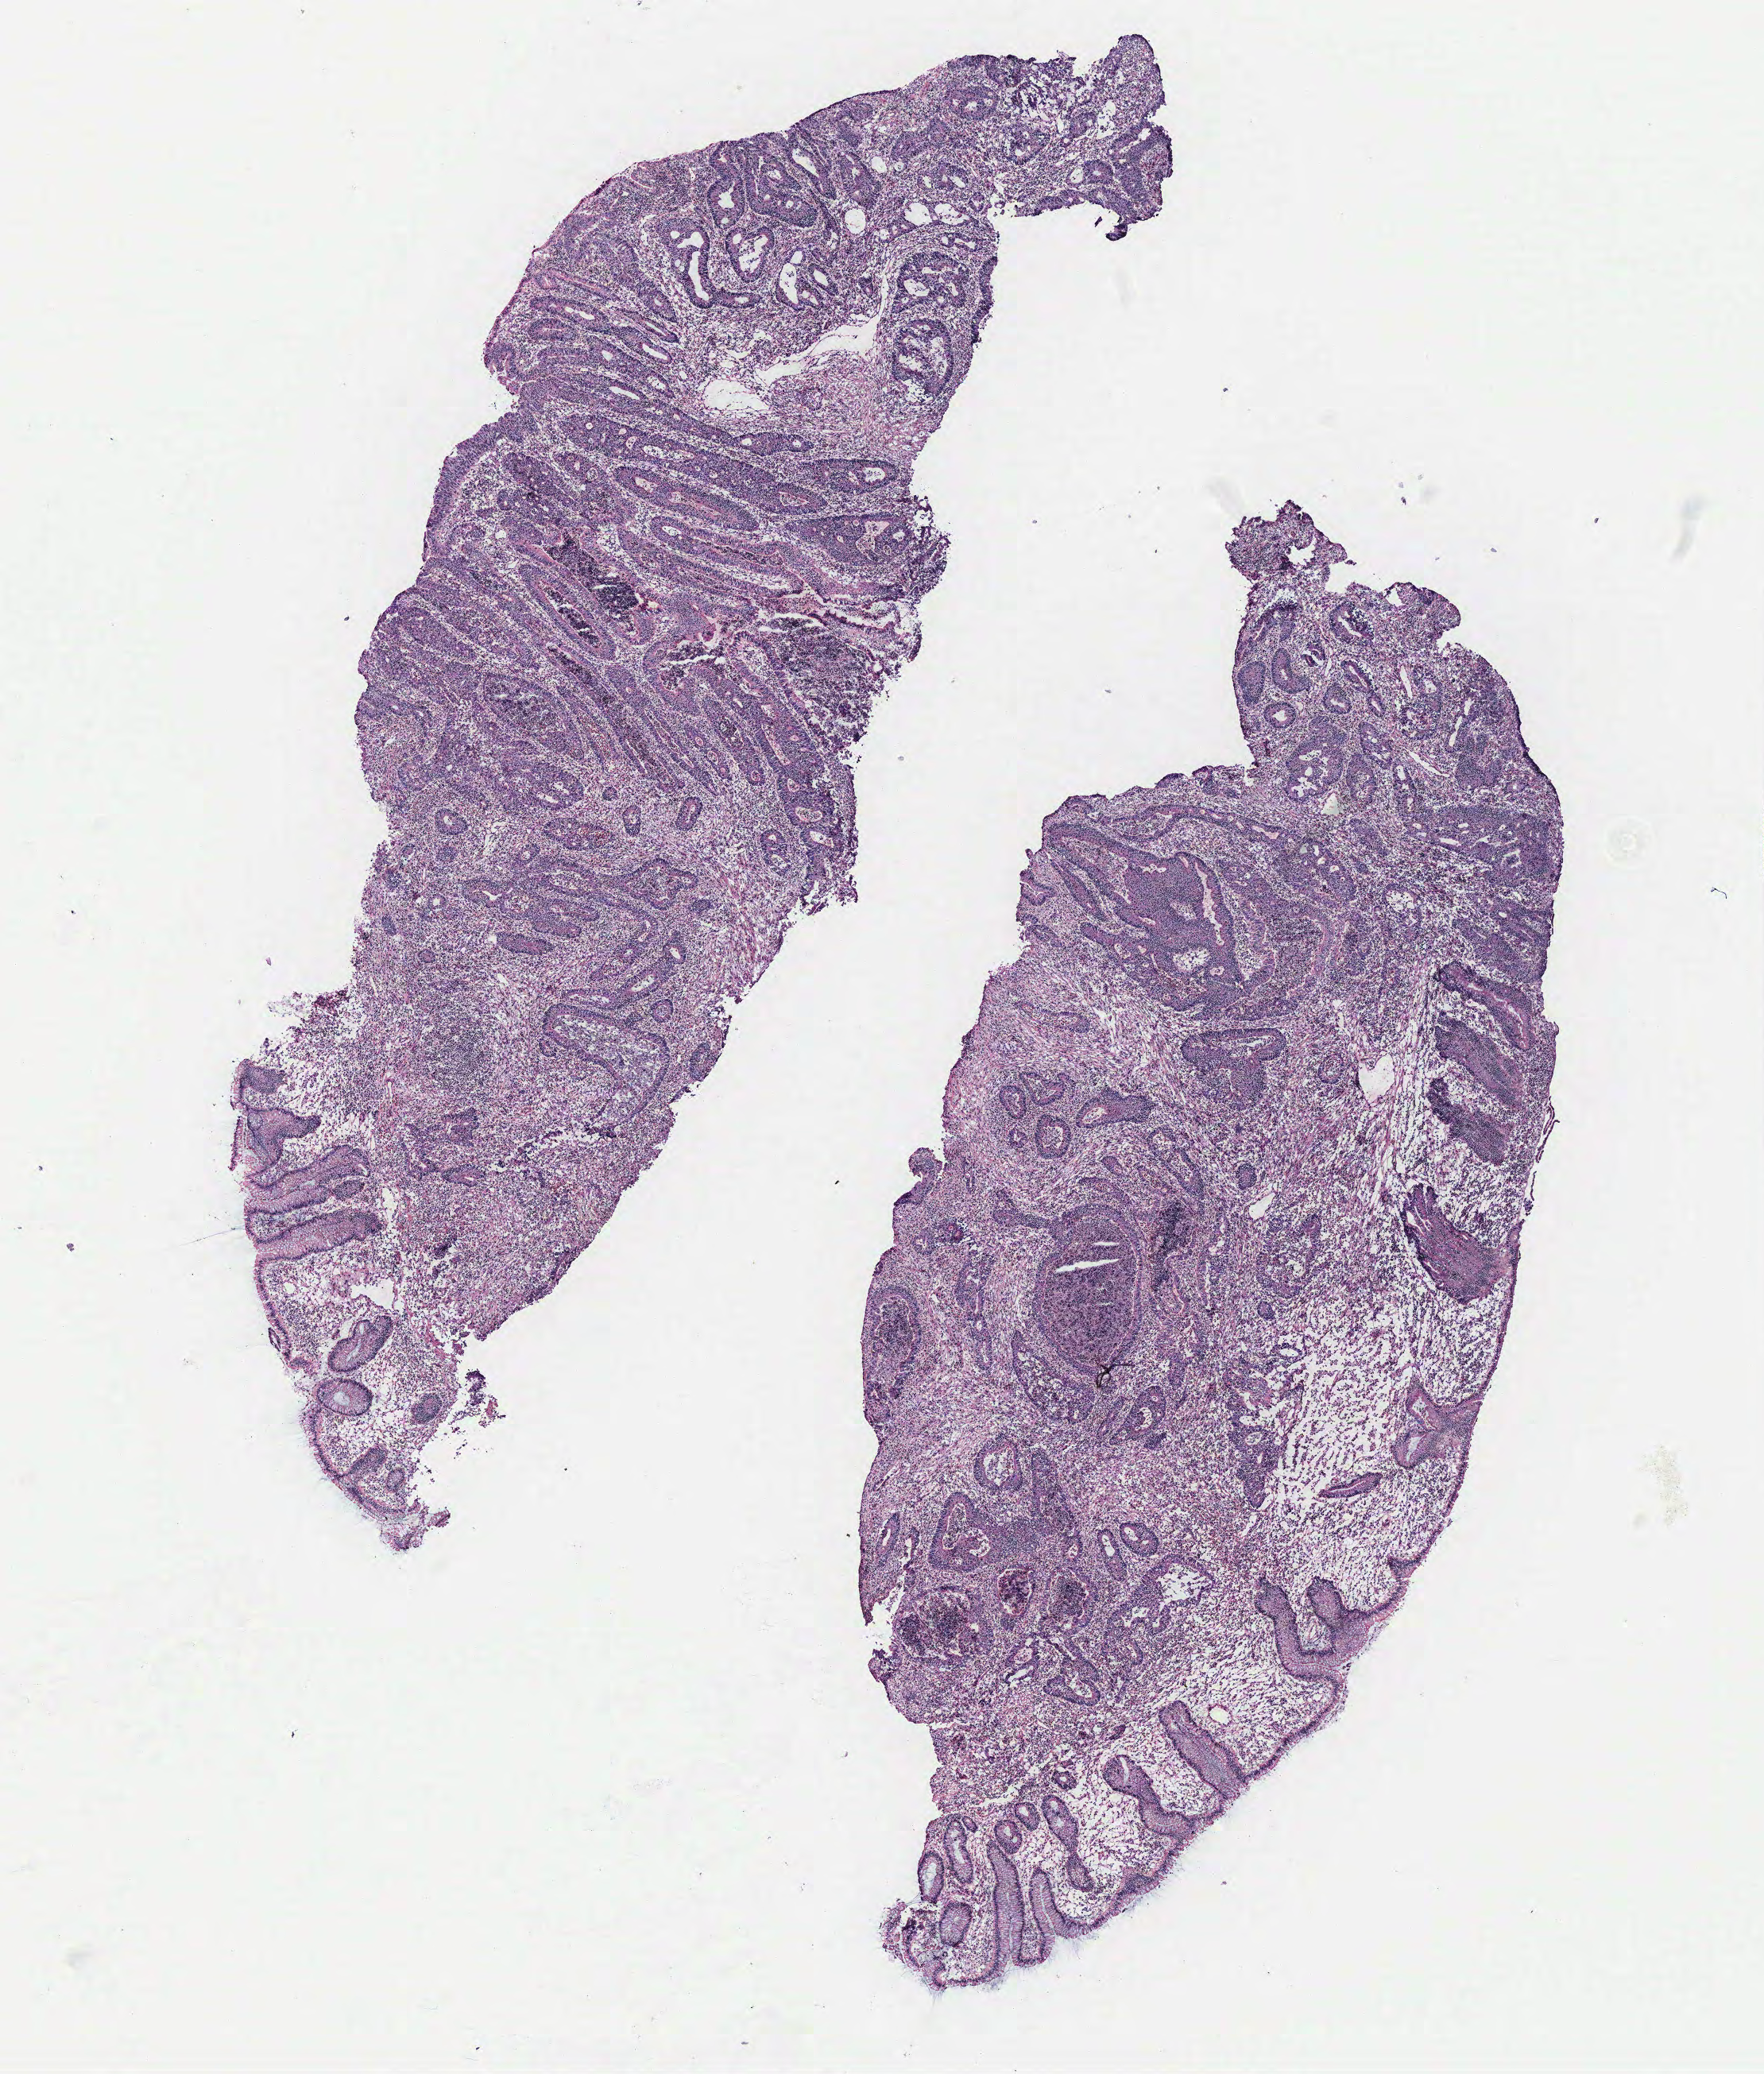
Digitized H&E-stained tissue section (whole slide), shown as a low-resolution overview of the whole scanned area (about 8.9 x 10.4 mm); colon, tissue type not recorded.
* patient diagnosis (cohort enrolment): colon cancer (colon)